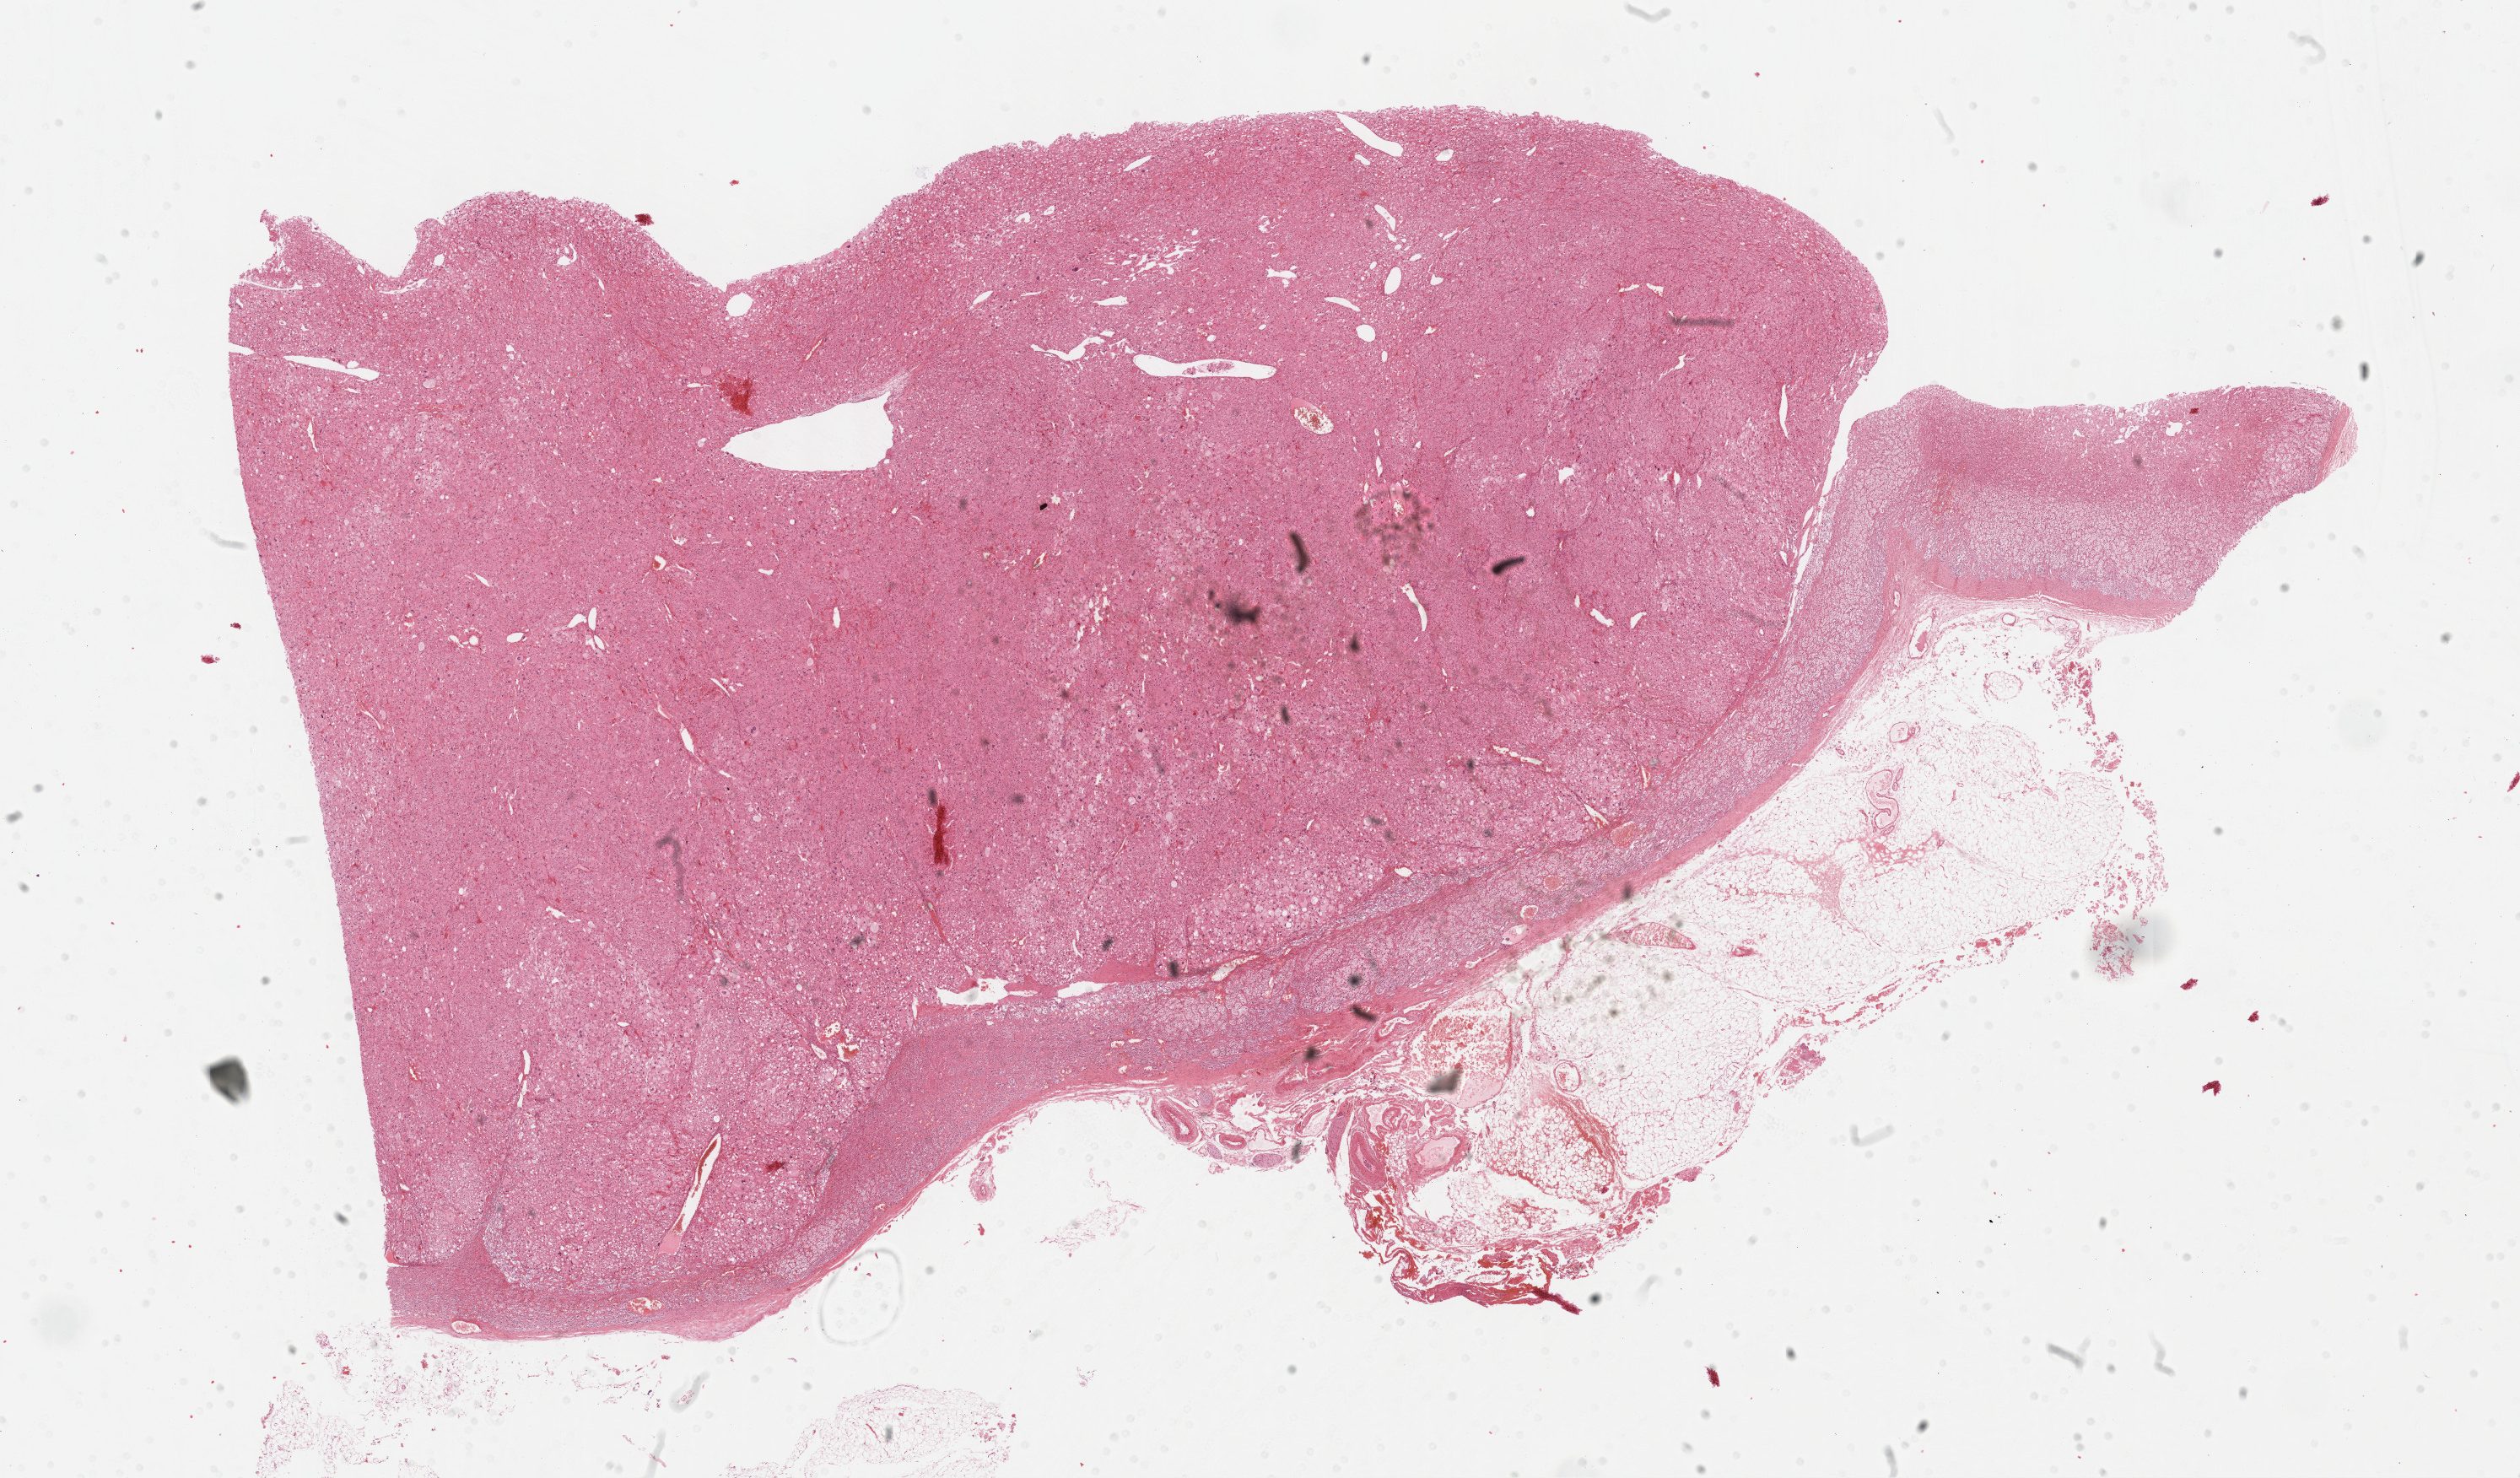
Whole-slide histology image, H&E-stained — shown as a low-resolution overview of the whole scanned area (about 24.2 x 14.2 mm, slide scanned at 40x), formalin-fixed paraffin-embedded (FFPE) diagnostic section, sample: primary tumour, adrenal cortex. Female patient; age at initial diagnosis 36 years.
Pathologic diagnosis: Adrenal cortical carcinoma.